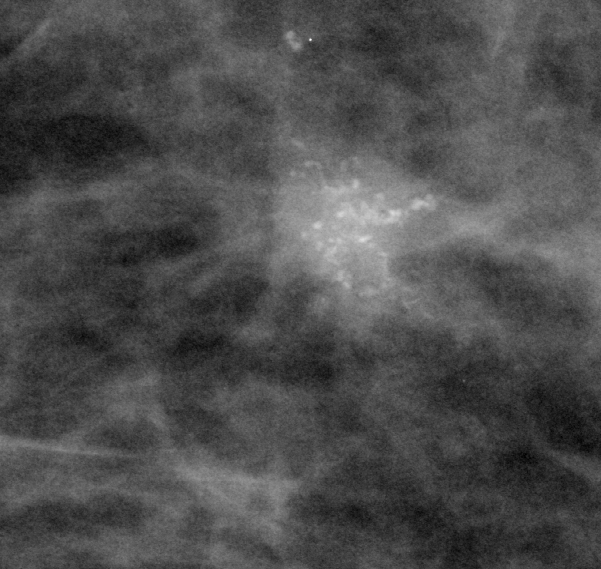
Crop from a digitized film mammogram around one marked abnormality; left breast; MLO view.
Calcifications, morphology pleomorphic, distribution clustered; BI-RADS assessment category 5; pathology (as recorded): malignant.